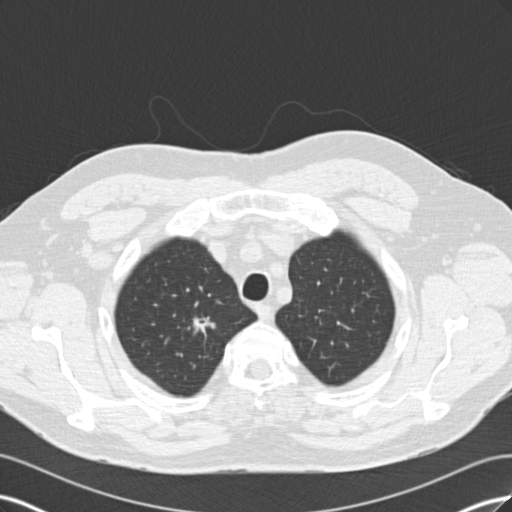
Low-dose screening chest CT, one axial slice. Slice 147 of 171 in the series (ordered by position). Reconstruction kernel B30f. 120 kVp. Lung window (W 1500 / L -600 HU). 2 mm slice thickness. 512 × 512 image matrix.
Outlined on this slice (manually delineated by an expert):
- lesion 1 (tumor, upper lobe of right lung): bounding box <188,317,216,338> (left, top, right, bottom; pixels)